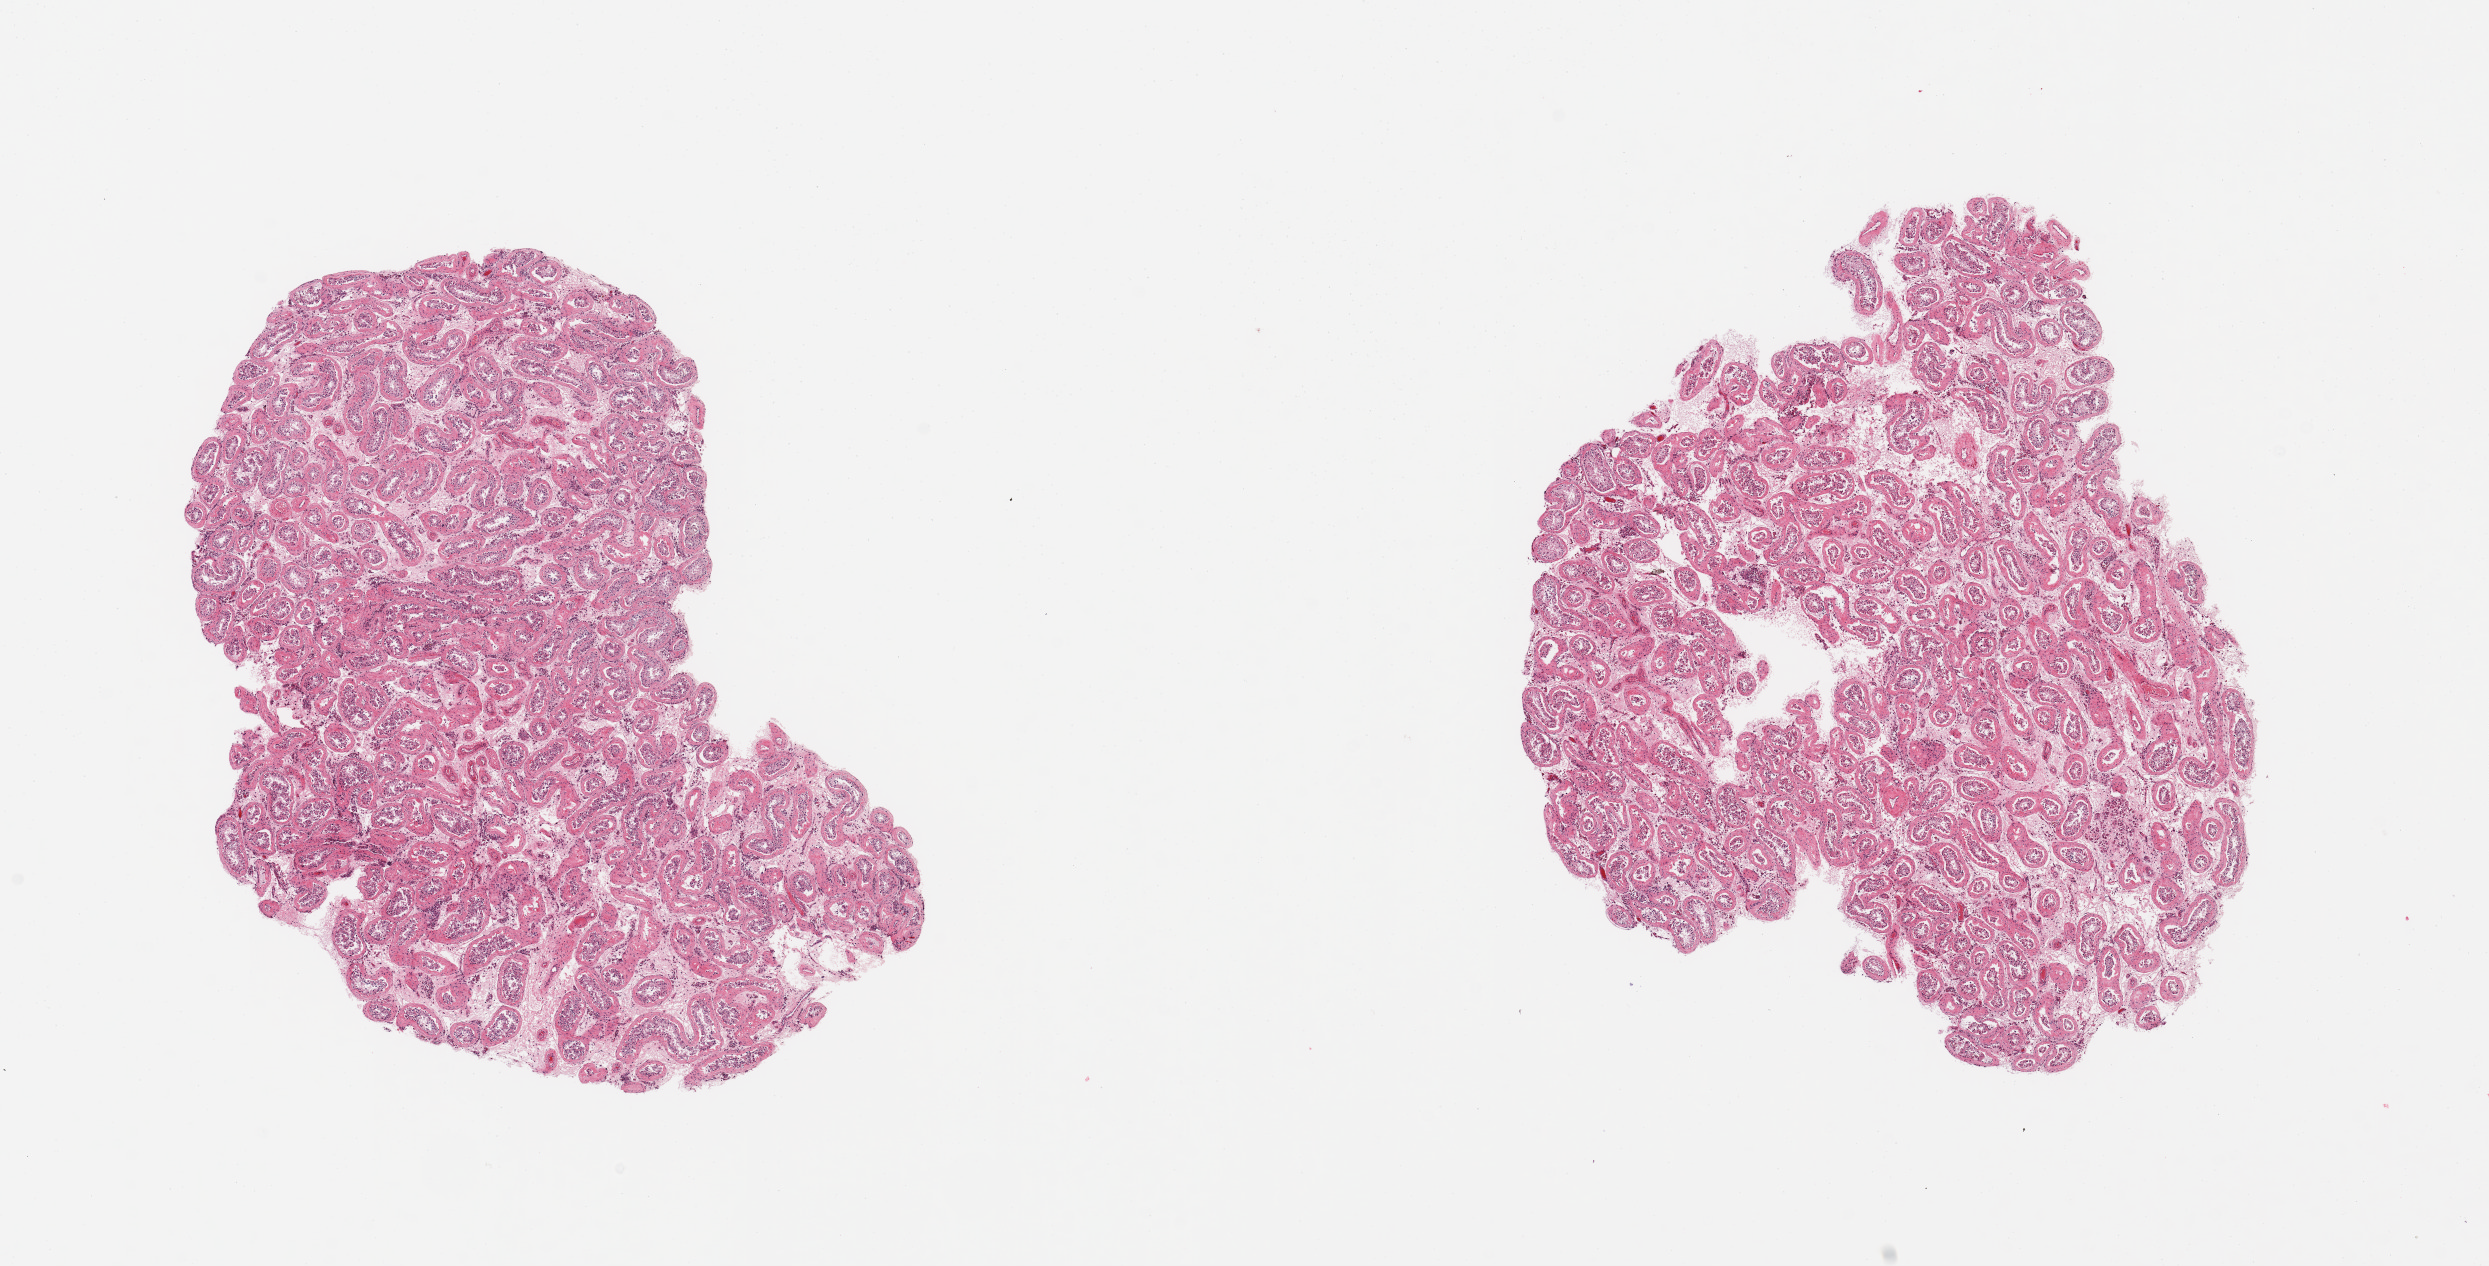
H&E whole-slide image, a low-resolution overview of the entire scanned area, about 19.7 x 10.0 mm. PAXgene-fixed, paraffin-embedded tissue. Target tissue: testis. Tissue donor sample. Donor: male.
• reviewer comment on this tissue sample: 2 pieces, spermatogenesis markedly reduced/aspermia